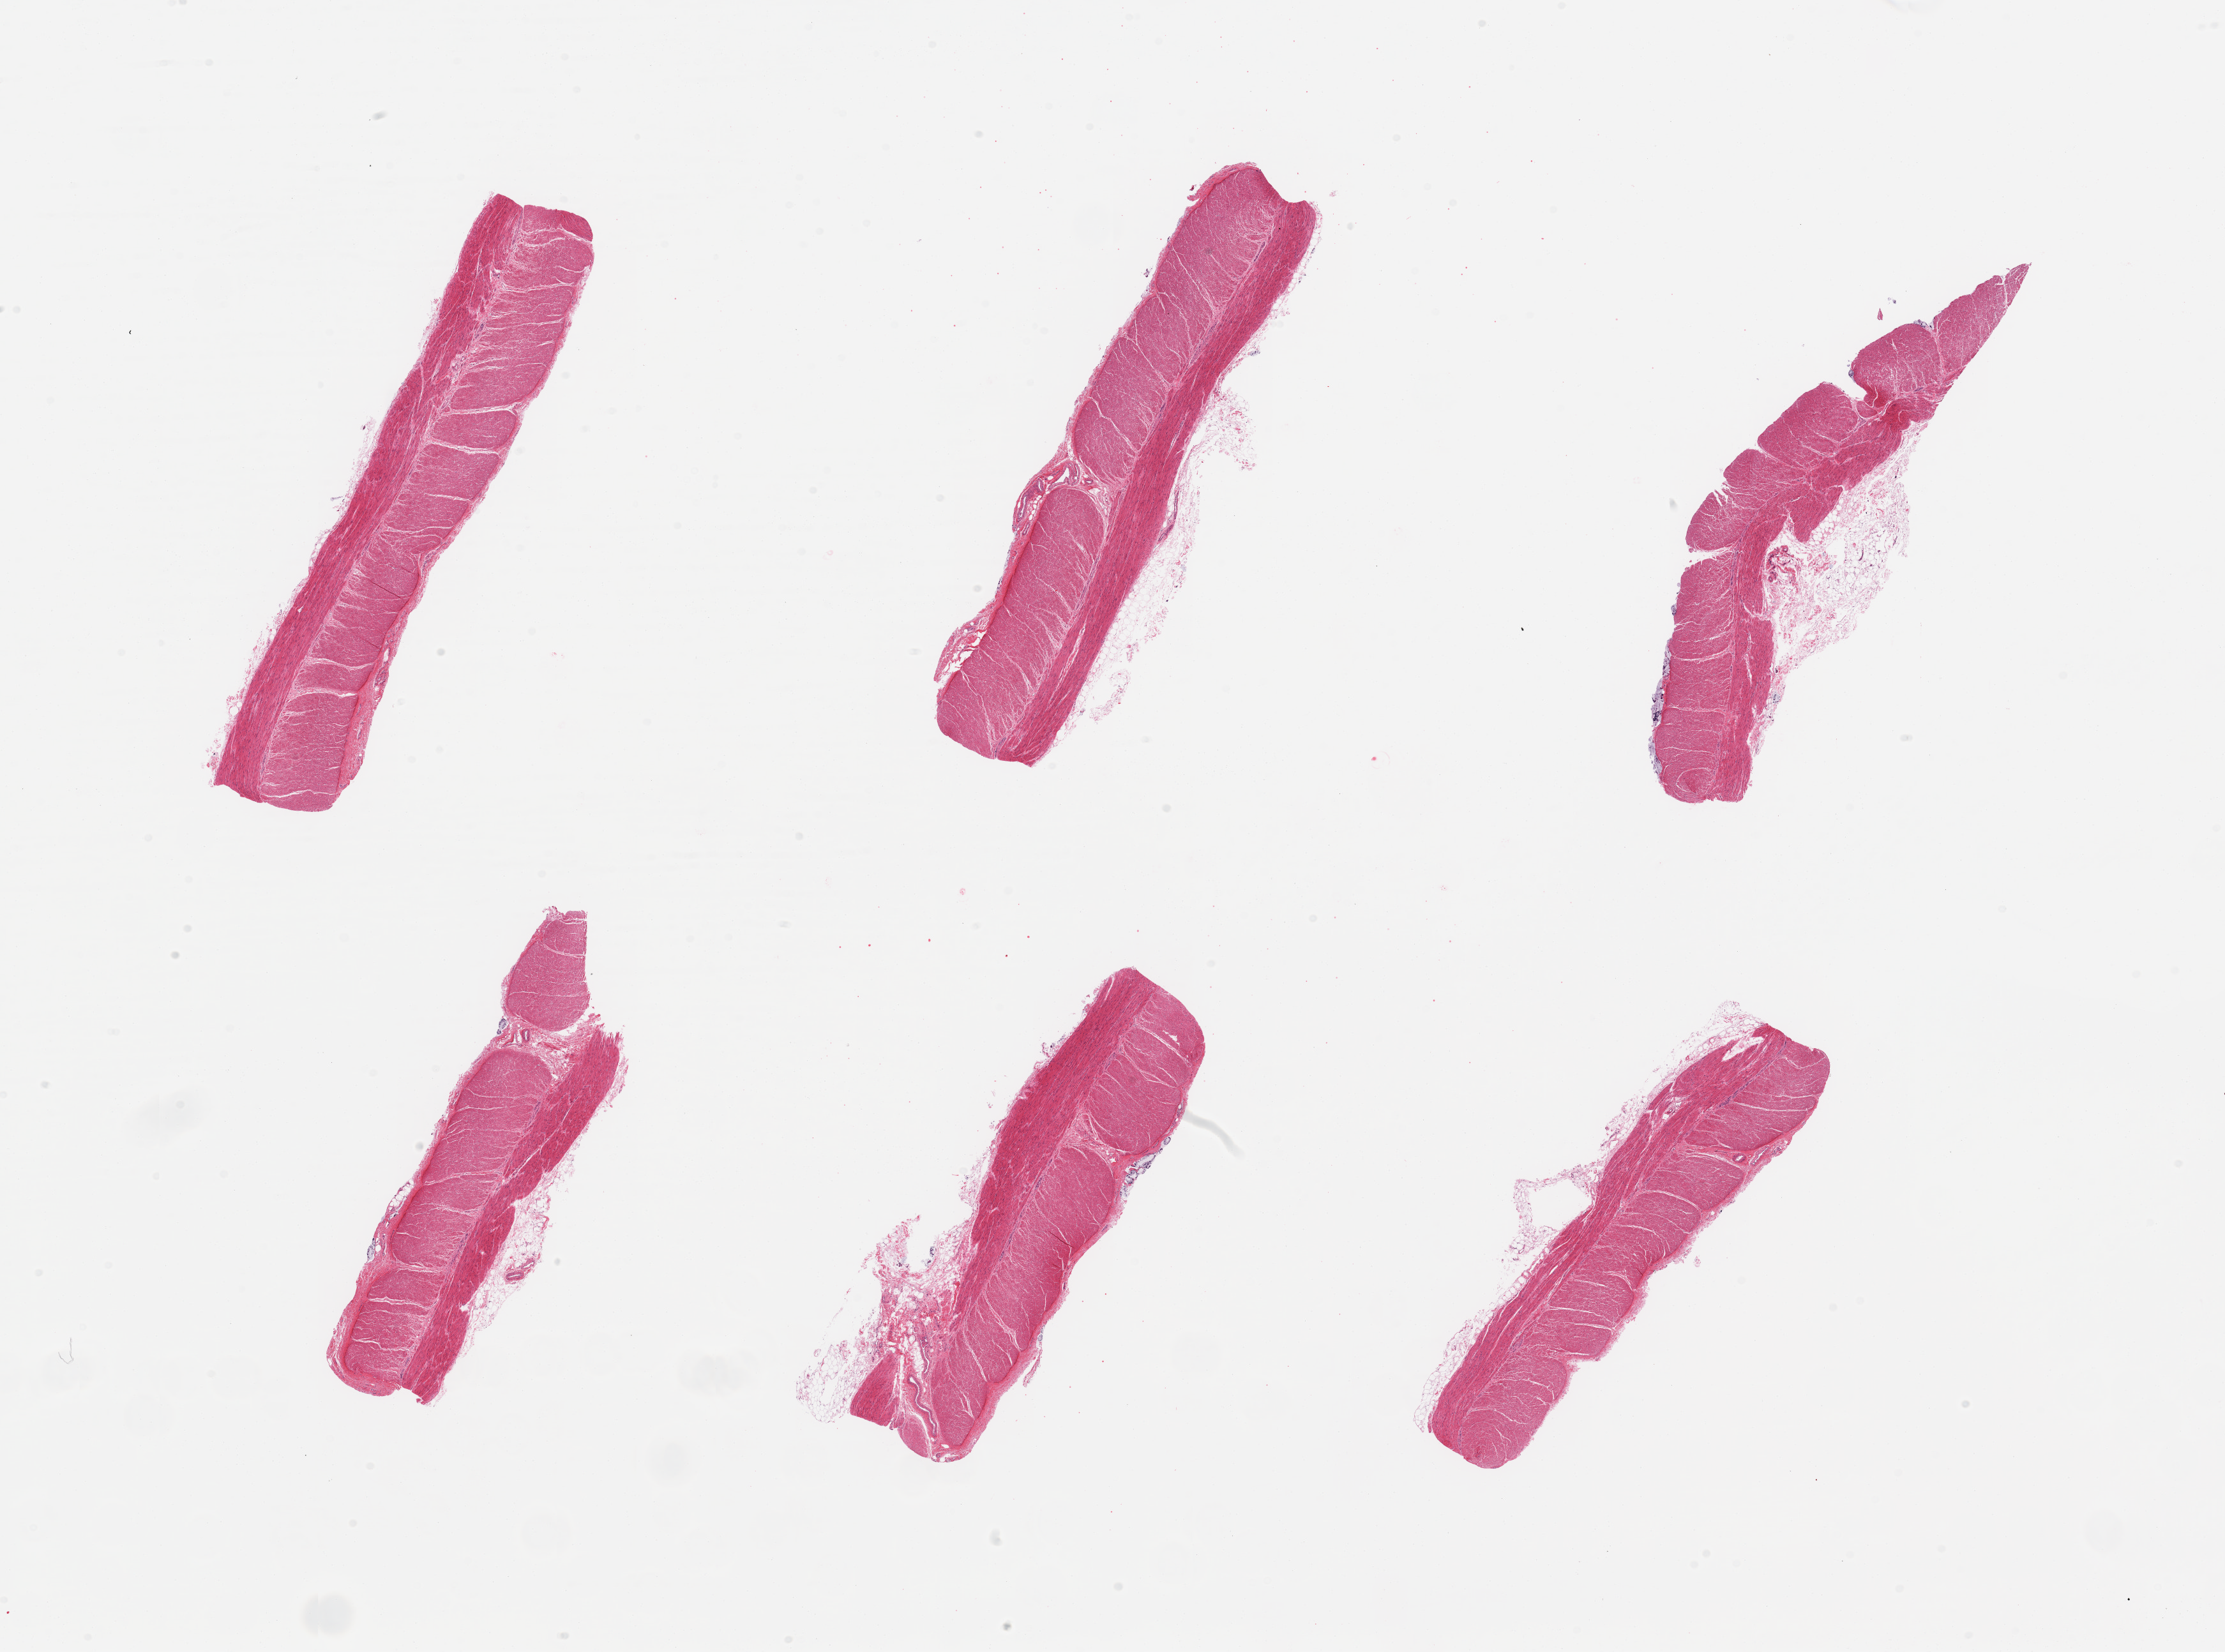
Hematoxylin and eosin (H&E) whole-slide image, whole scanned area (about 27.6 x 20.5 mm, slide scanned at 20x) shown as a low-resolution overview. PAXgene-fixed paraffin-embedded (PFPE) section. Target tissue: sigmoid colon. Donor tissue sample. Donor sex: female.
Reviewer comment on this tissue sample: 6 pieces, confirmed target muscularis, few trace nubbins of adherent fat.